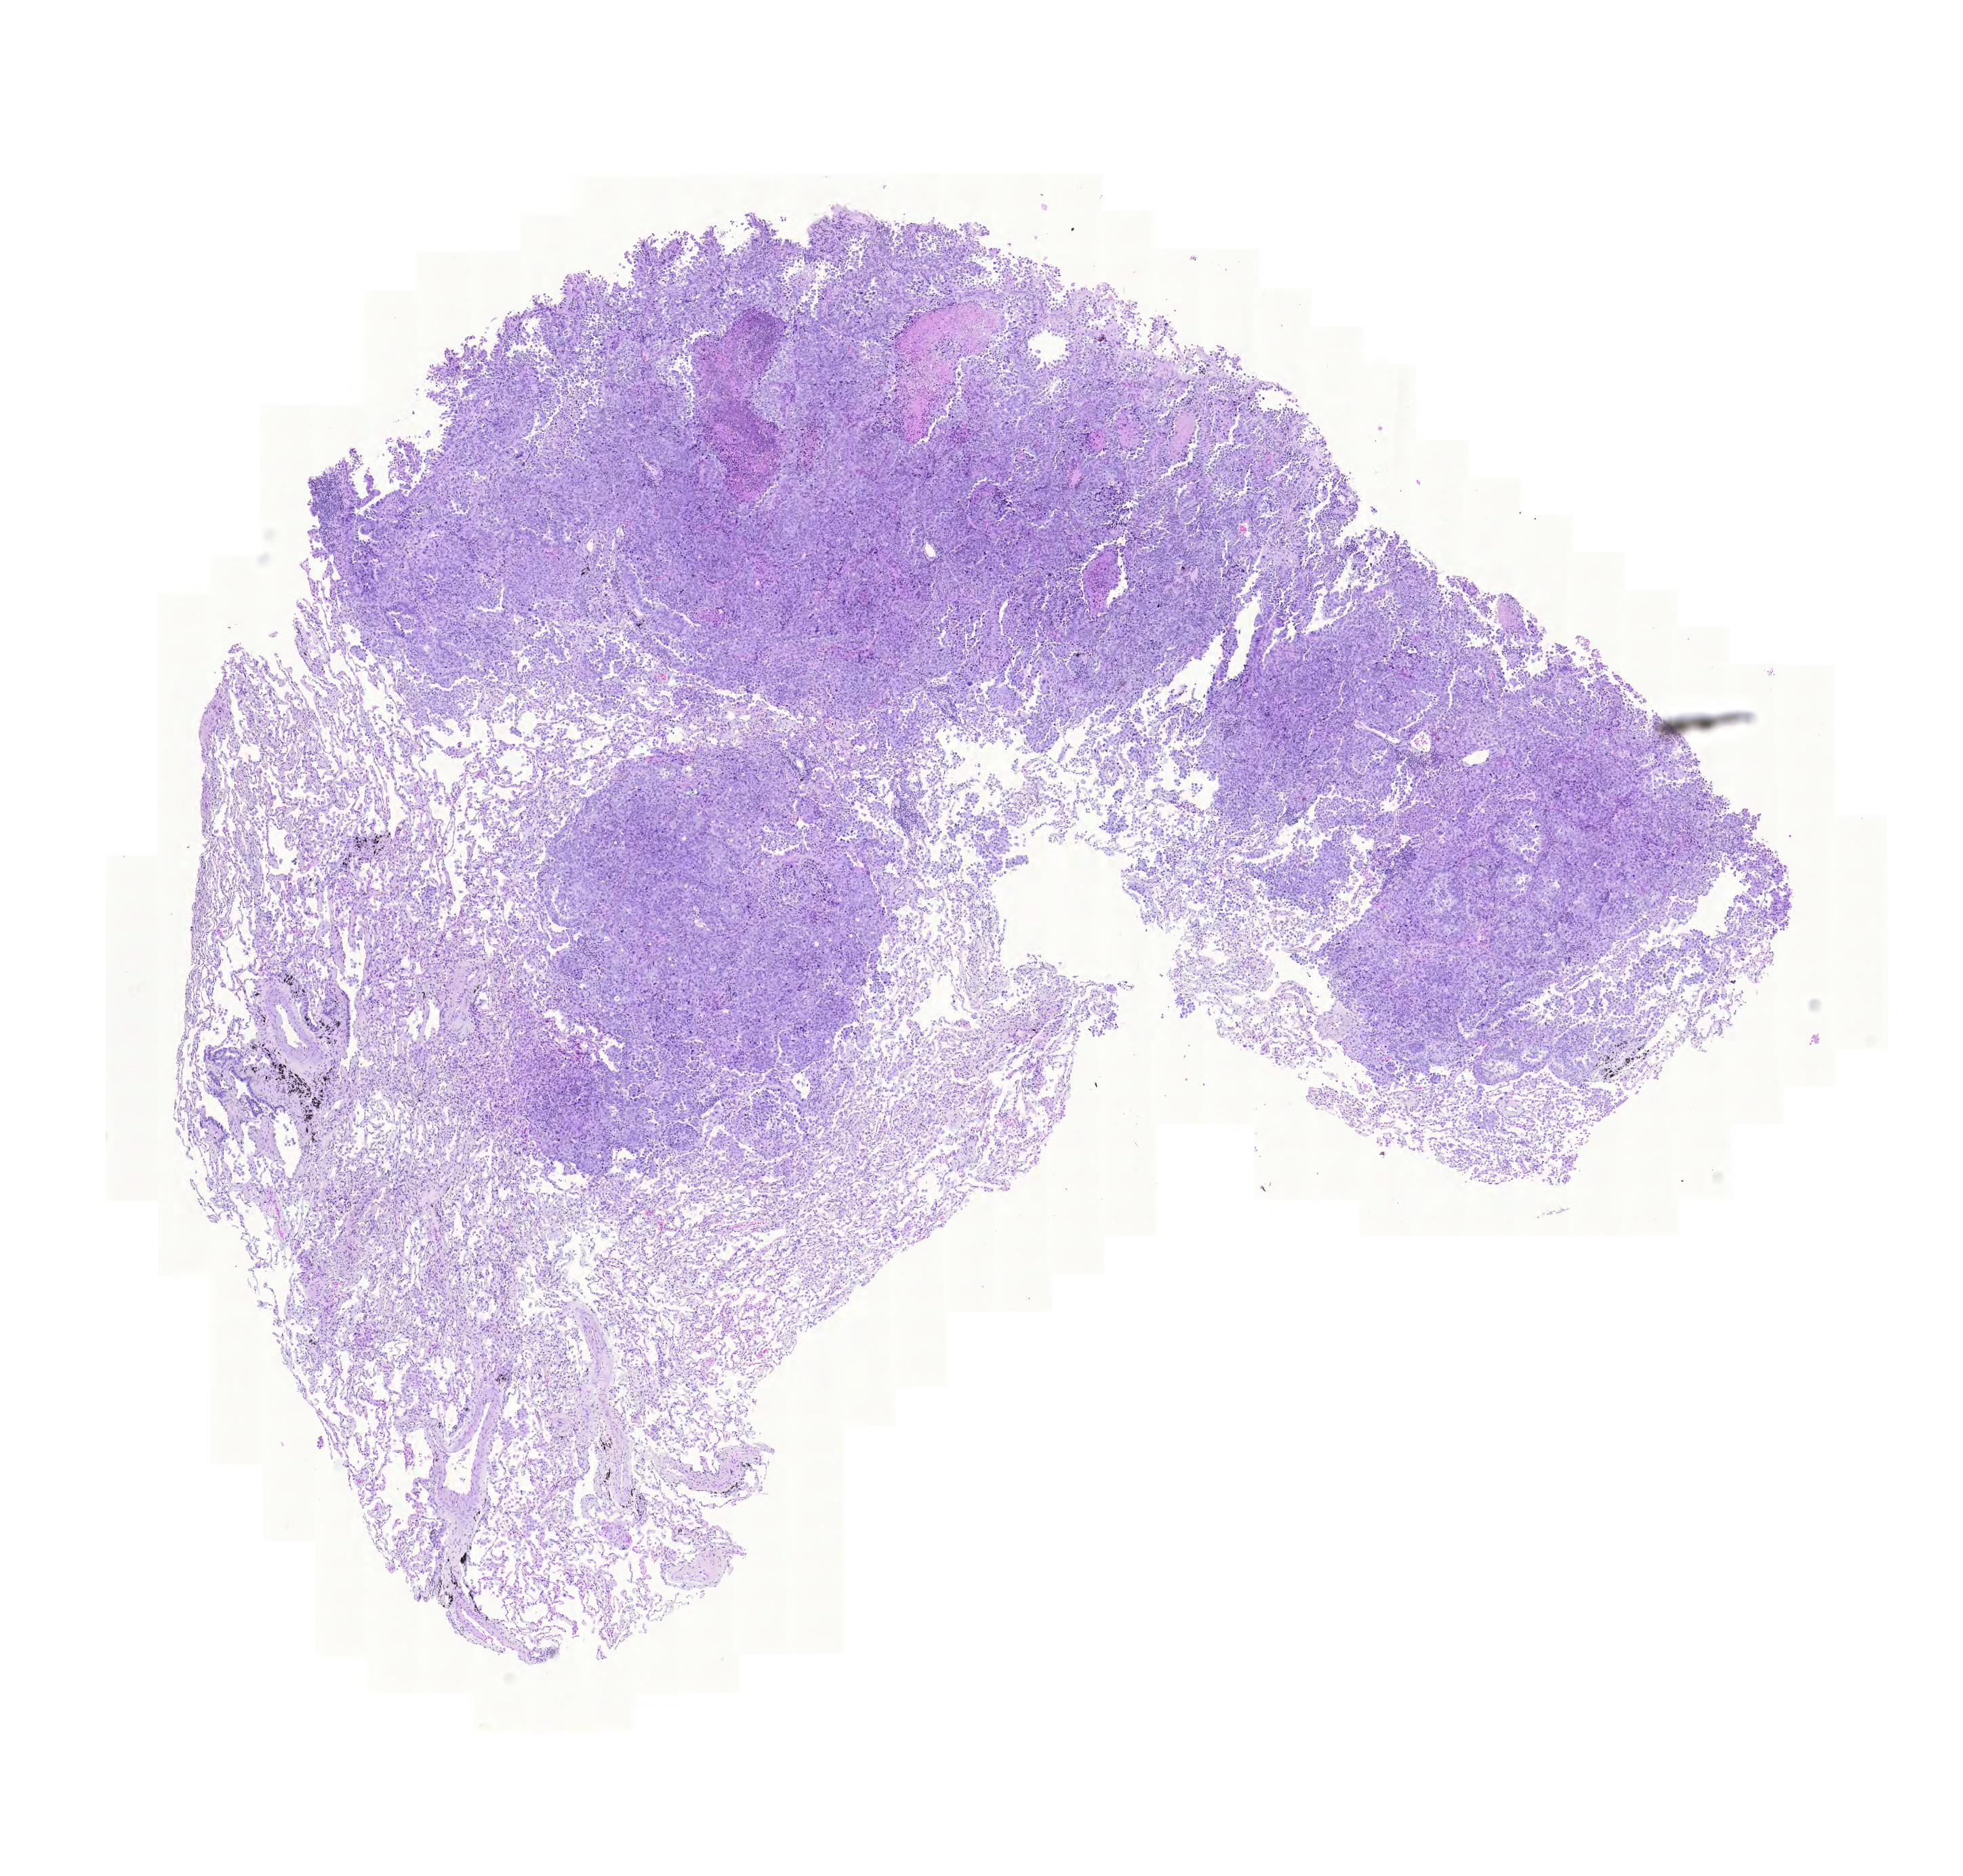
Whole-slide histology image, H&E-stained — shown as a low-resolution overview of the whole scanned area (about 10.8 x 10.3 mm); FFPE section; lung, primary tumour sample. Male, age 70 years at initial diagnosis.
Diagnosis: Adenocarcinoma, NOS (lower lobe, lung).